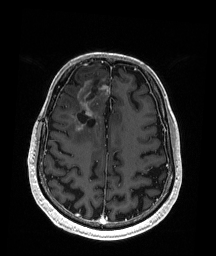
Brain MRI from a brain-tumour surgery series, one axial slice. Position 63 of 192 along the scan axis. T1-weighted post-contrast. 1 mm slice thickness. 216 × 256 image matrix, field of view 211 × 250 mm. From the clinical record (not read from this slice): histopathology: Astrocytoma; WHO grade: 3; IDH mutation: yes; tumour location: Right Frontal.
Annotated regions visible in this slice (expert manual segmentation):
- previous resection cavity: bounding box <78,79,100,124> (left, top, right, bottom; pixels)
- tumour: <71,81,109,136>